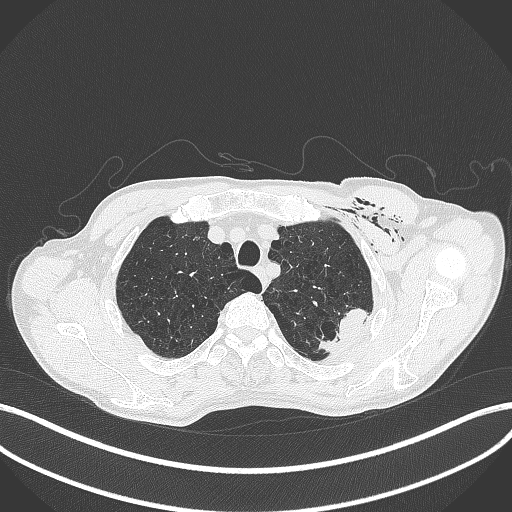
Chest CT, one axial slice; slice 351 of 457 in the series (ordered by position); lung window (W 1500 / L -600 HU); 512 × 512 image matrix, field of view 400 × 400 mm. Patient: male, 58 years. From the clinical record (not read from this slice): clinical TNM (as recorded): T3 N0 M0.
Outlined on this slice (rectangle marked by the reading radiologist):
- lung tumour (recorded histology: adenocarcinoma): bounding box <315,301,369,354> (left, top, right, bottom; pixels)